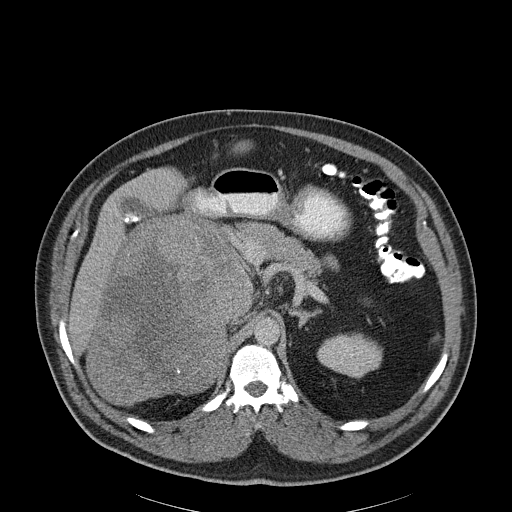
Contrast-enhanced abdominal CT, one axial slice. Position 132 of 186 along the scan axis. Soft-tissue window (W 400 / L 40 HU). 3 mm slice thickness. 512 × 512 image matrix, field of view 464 × 464 mm. Male patient, age 56 years. From the clinical record (not read from this slice): diagnosis: adrenocortical carcinoma; tumour side: right adrenal; tumour size at pathology: 18 cm; Ki-67 index: 2 %; stage (as recorded): 3.
Outlined on this slice (semi-automatic segmentation, software-assisted and operator-edited):
- mass: bounding box [x1, y1, x2, y2] px = [89, 219, 251, 402]